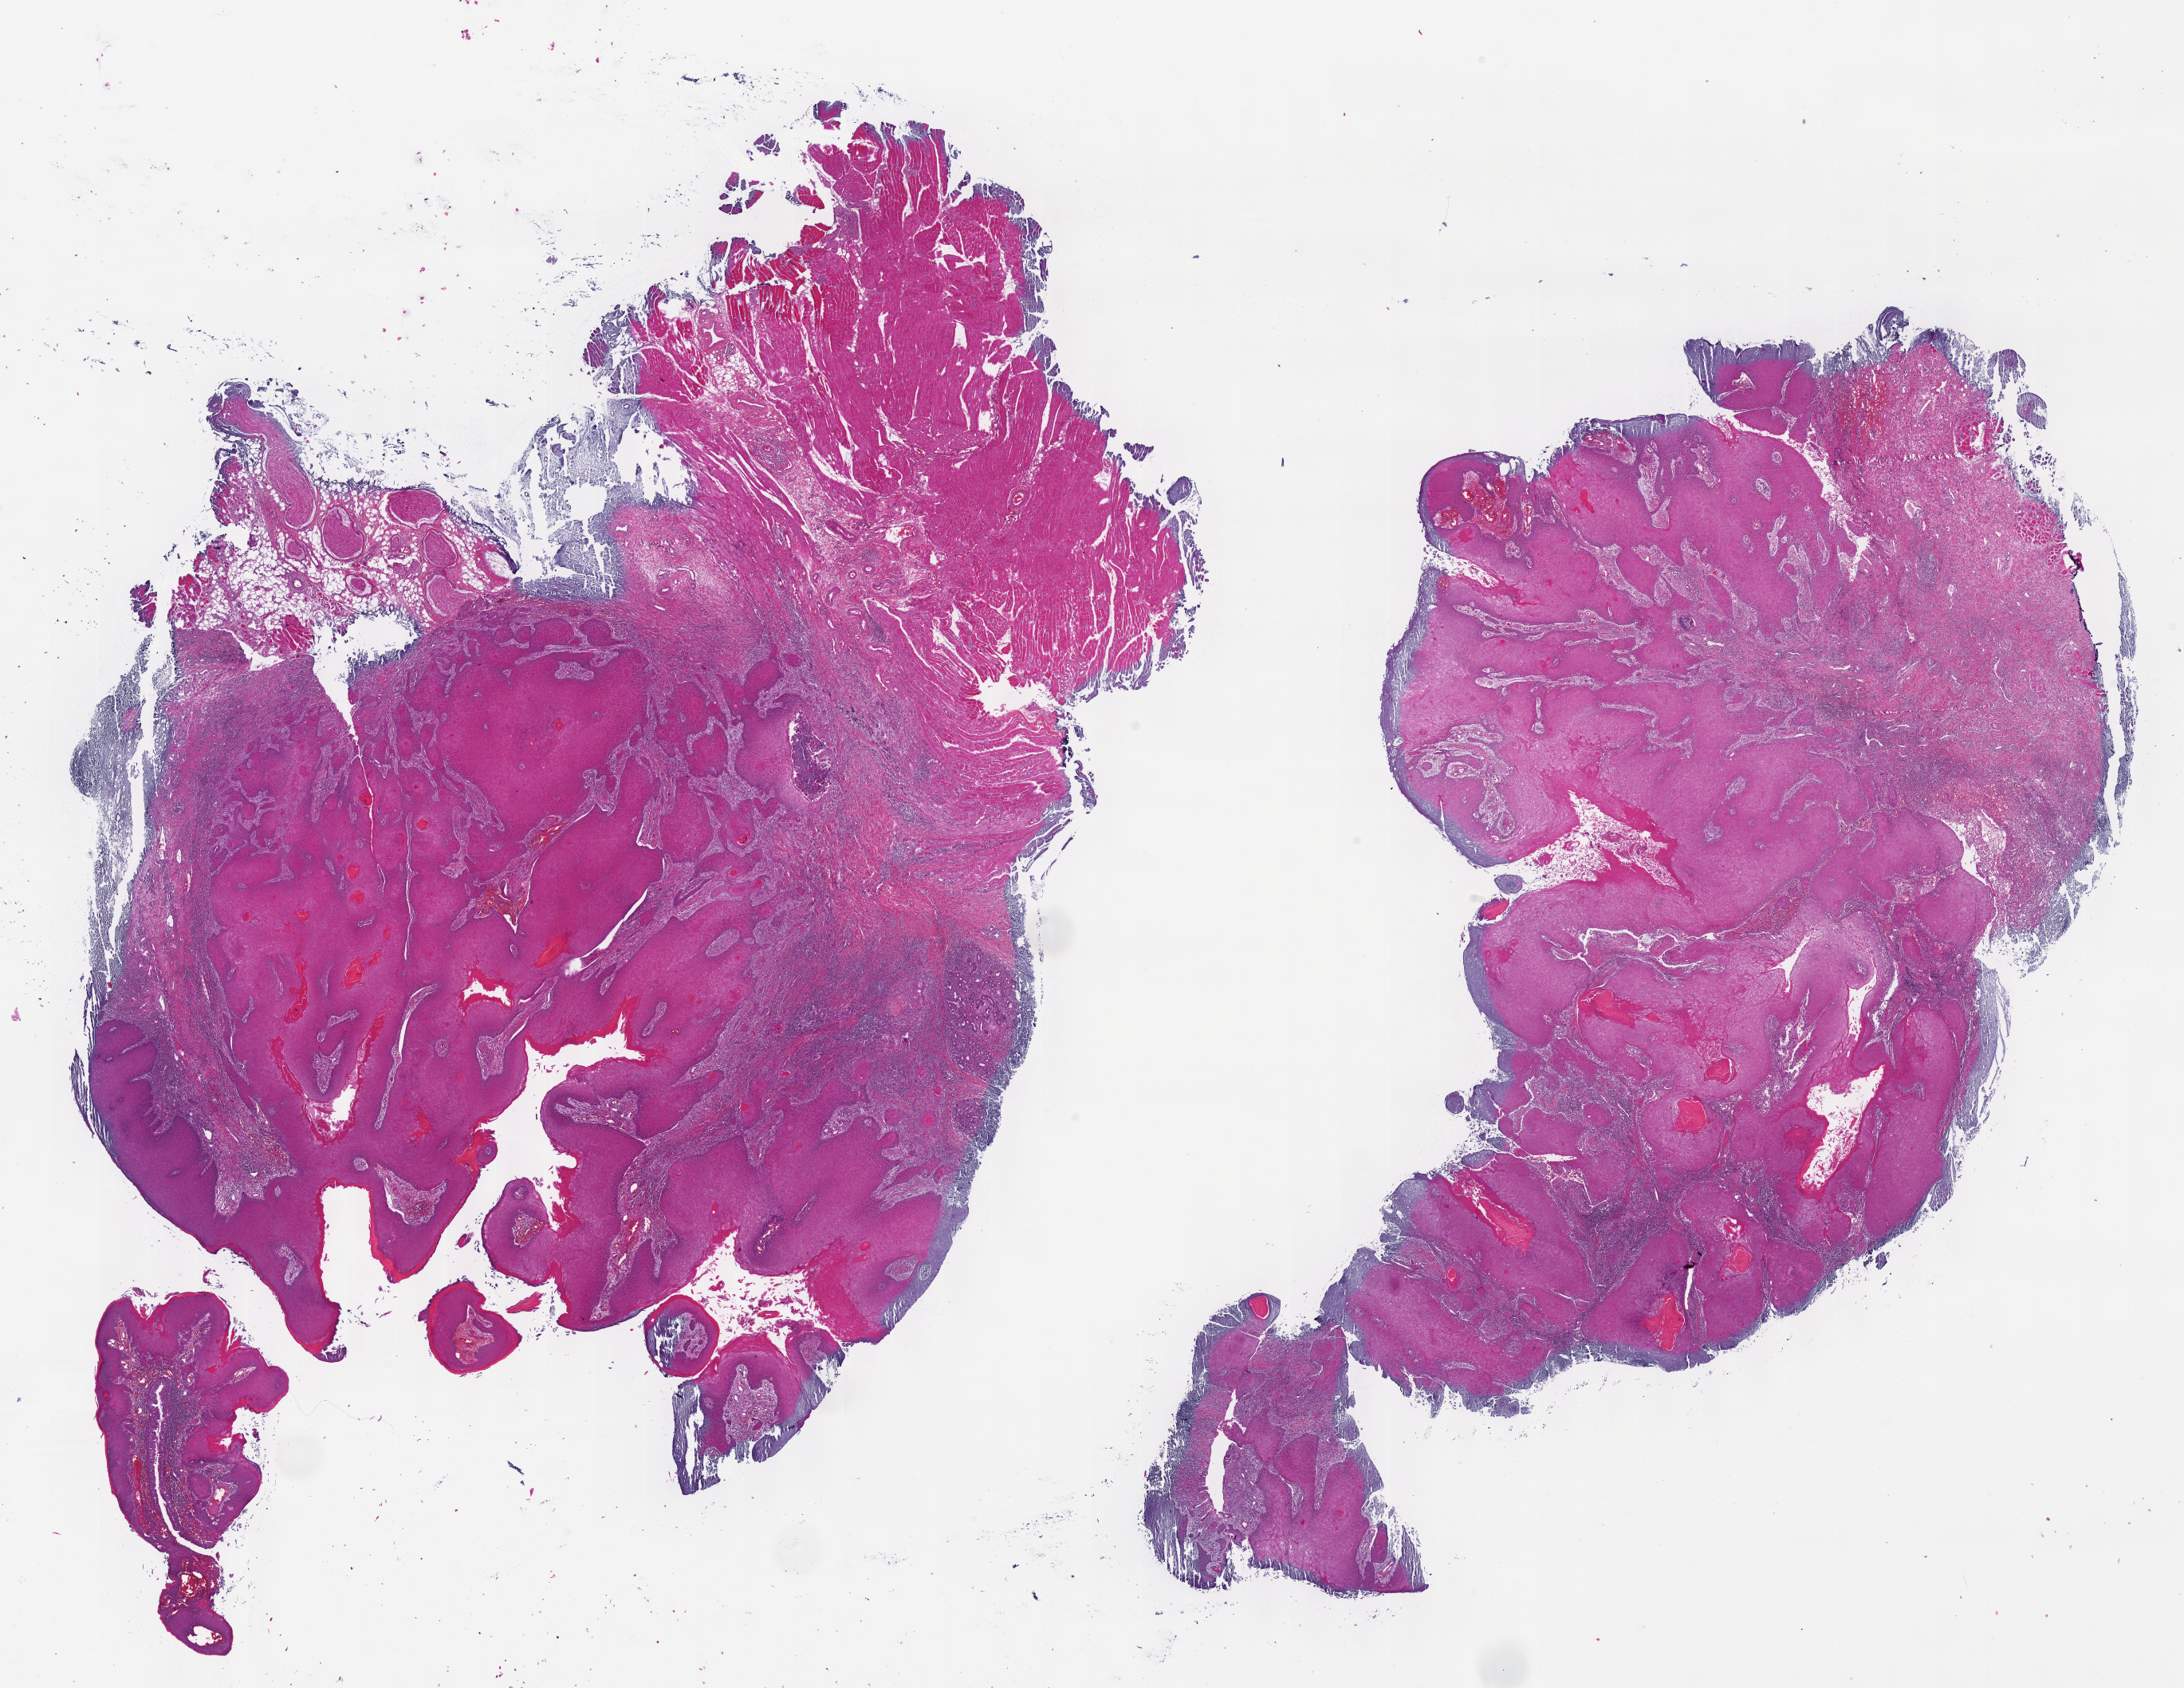
H&E-stained whole-slide image, whole scanned area (about 22.1 x 17.1 mm, from a 40x scan) shown as a low-resolution overview. FFPE section. Primary tumour sample from the head and neck. Female patient; age at initial diagnosis 64 years.
Diagnosis: Squamous cell carcinoma, NOS (overlapping lesion of lip, oral cavity and pharynx).